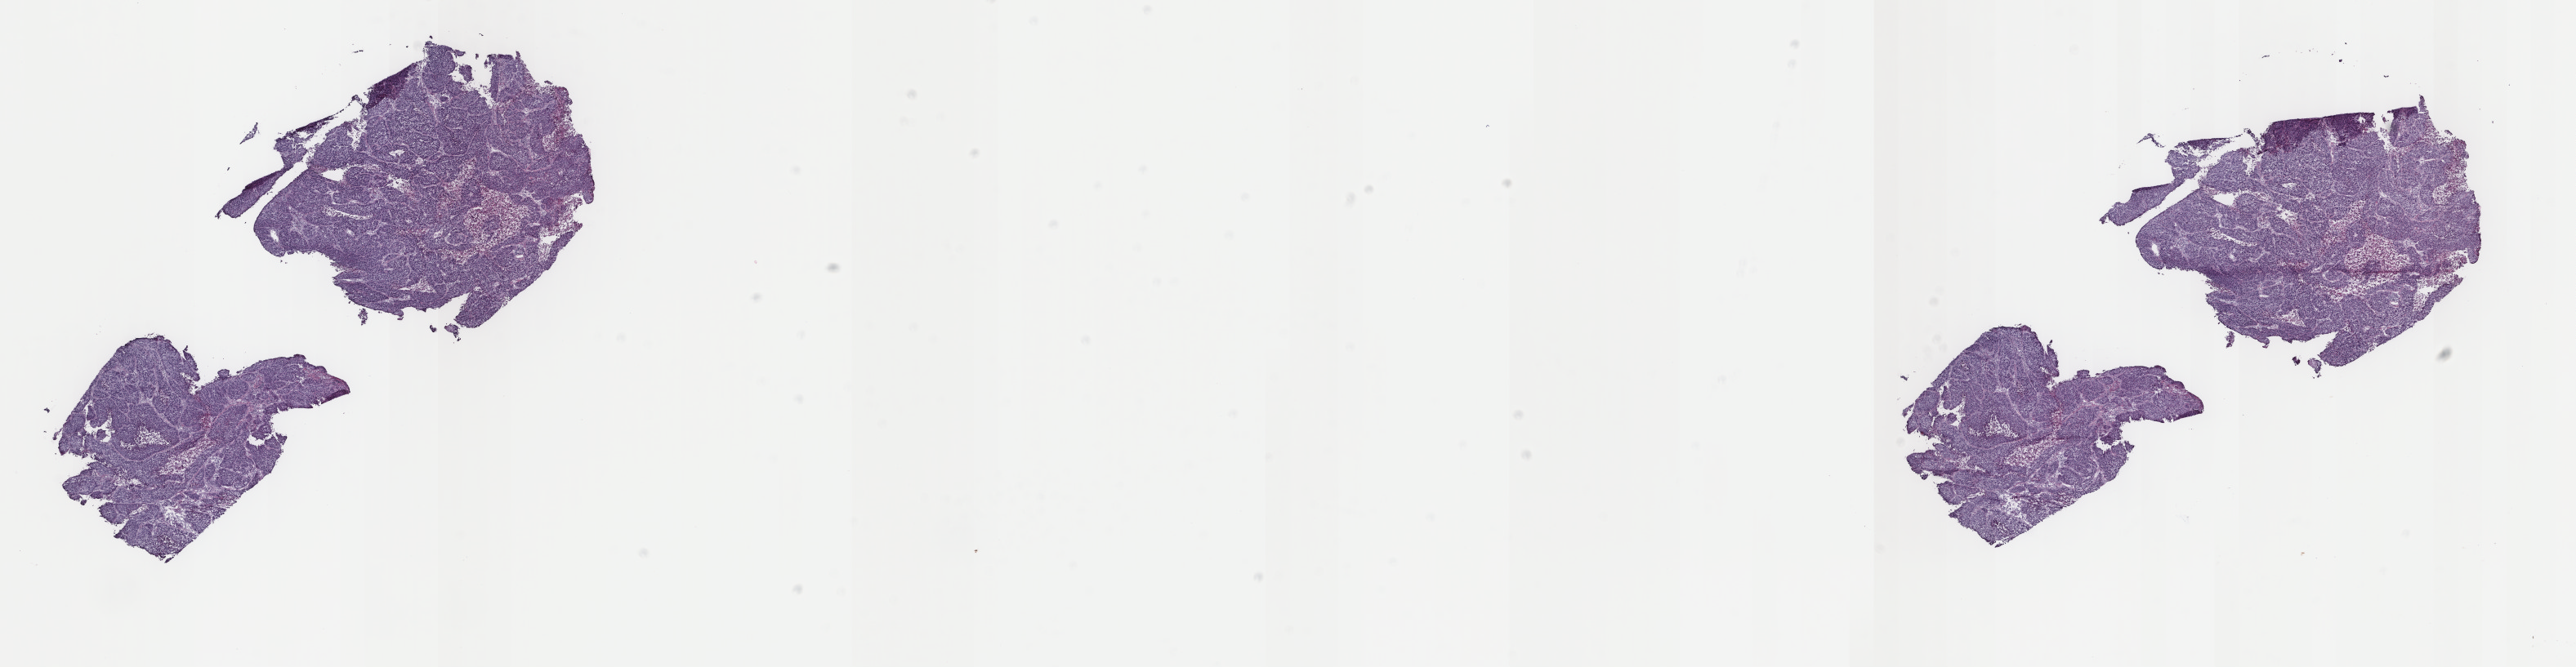
Digitized H&E-stained tissue section (whole slide), a low-resolution overview of the entire scanned area, about 25.0 x 6.5 mm (acquisition: 40x scan), frozen section from the top of the tissue portion, cervix, primary tumour sample. Female, age 51 years at initial diagnosis. Histologic grade: G2 (moderately differentiated). Slide review estimates, as recorded: tumour cells 80%, tumour nuclei 80%, normal cells 0%, stromal cells 10%, necrosis 10%. Inflammatory infiltration, as recorded: lymphocyte infiltration 30%, monocyte infiltration 0%, neutrophil infiltration 10%.
• pathologic diagnosis: Squamous cell carcinoma, NOS
• FIGO stage: IIB